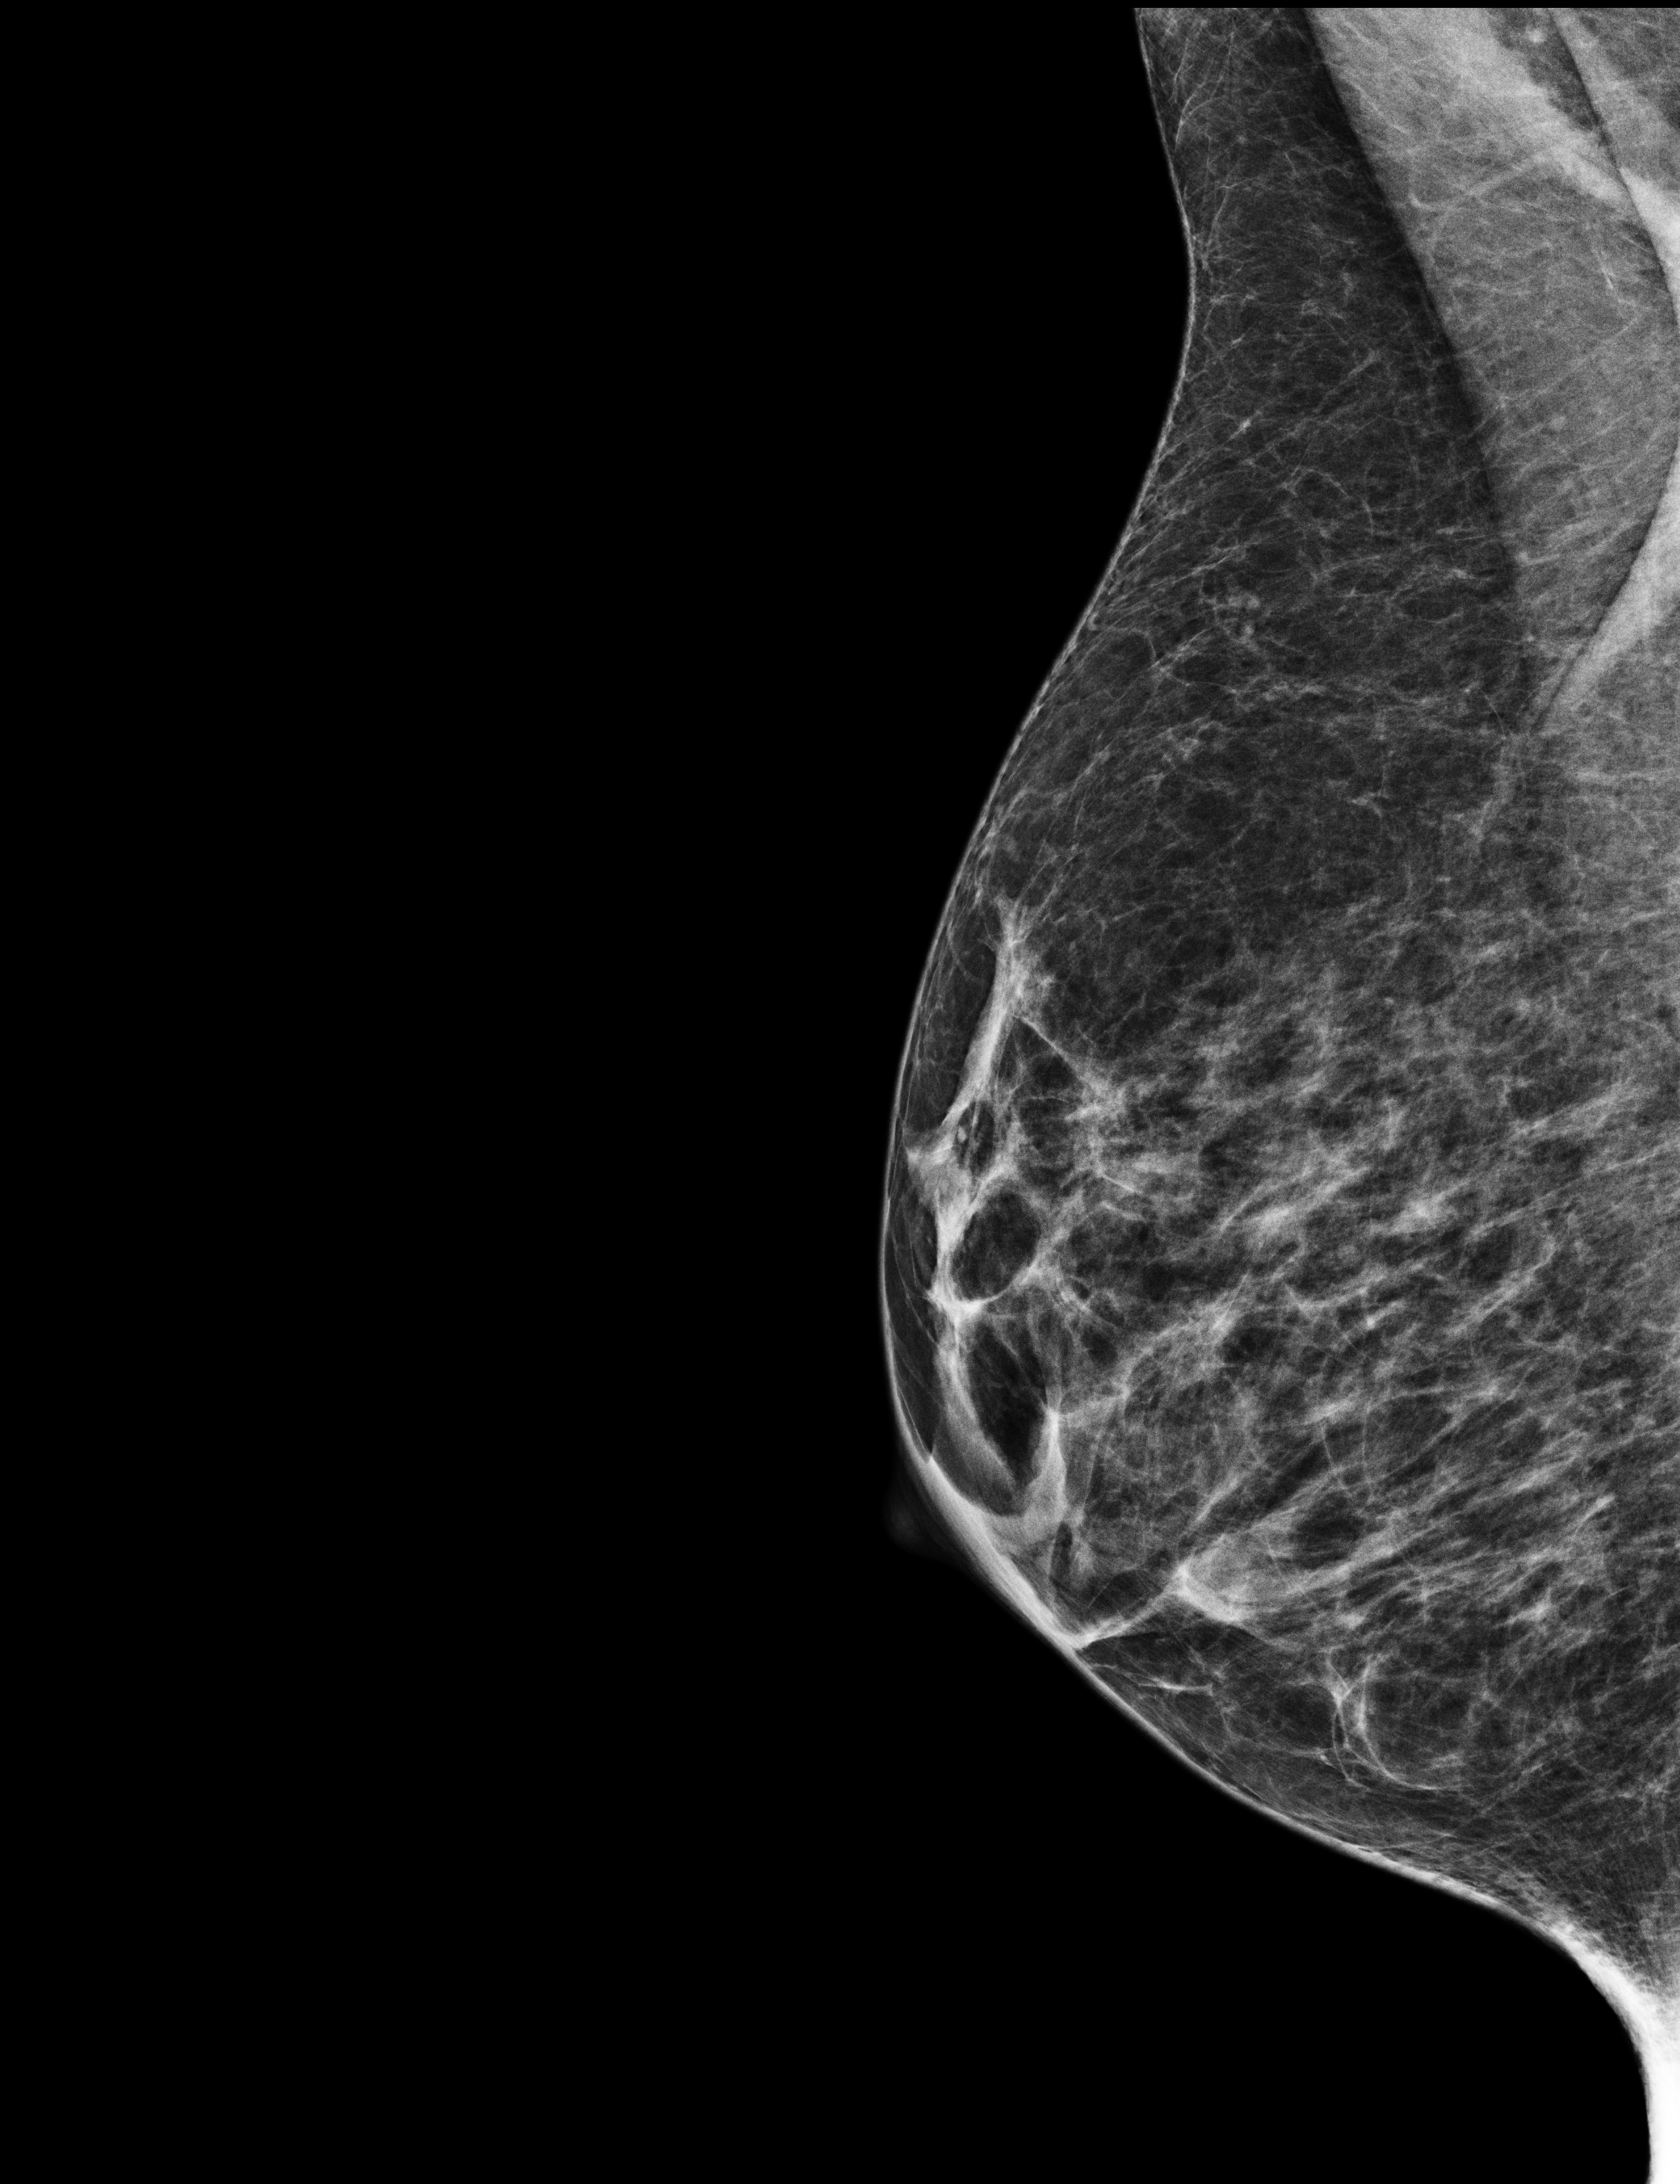
Digital mammogram (FFDM); right breast; mediolateral oblique (MLO) view; screening examination; compressed breast thickness 35 mm. Female patient, age 69 years.
- BI-RADS breast density category at the screening exam (both breasts, scale 1–4): 2
- final BI-RADS category for the screening round (tomosynthesis exam, both breasts): category 1
- recall: no recall after this screen